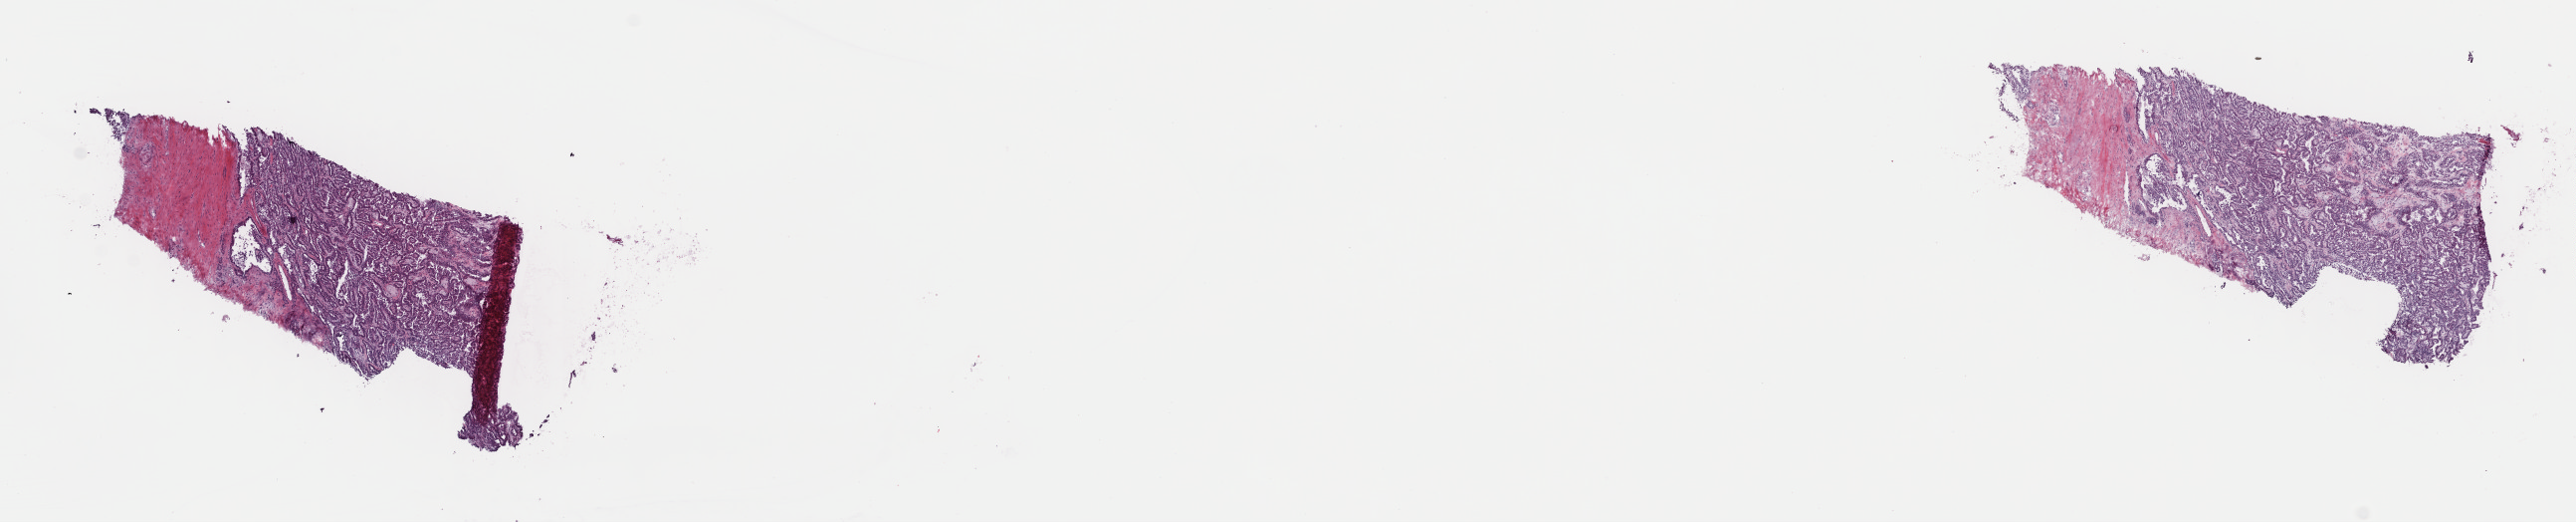
Whole-slide histology image, H&E-stained — a low-resolution overview of the entire scanned area, about 20.4 x 4.1 mm. Frozen section. Primary tumour sample from the kidney. Patient: female, age at initial diagnosis 80 years. Slide review estimates, as recorded: tumour cells 74%, tumour nuclei 80%, normal cells 0%, stromal cells 25%, necrosis 1%. Inflammatory infiltration, as recorded: lymphocyte infiltration 3%, monocyte infiltration 10%, neutrophil infiltration 0%.
Pathologic diagnosis: Papillary adenocarcinoma, NOS. AJCC pathologic stage: I (7th edition).